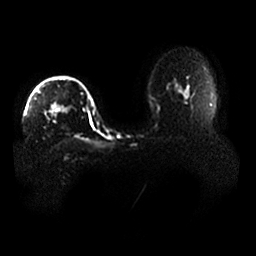
Breast MRI, one axial slice. Position 32 of 33 along the scan axis. Diffusion-weighted series; image 2 of 4 stored at this slice position (different b-values; order by instance number). 1.5 T. 4 mm slice thickness. 256 × 256 image matrix. Female patient.
Outlined on this slice (outlined manually by an expert reader):
- tumour on diffusion-weighted imaging: box from (x=57, y=105) to (x=70, y=115) px